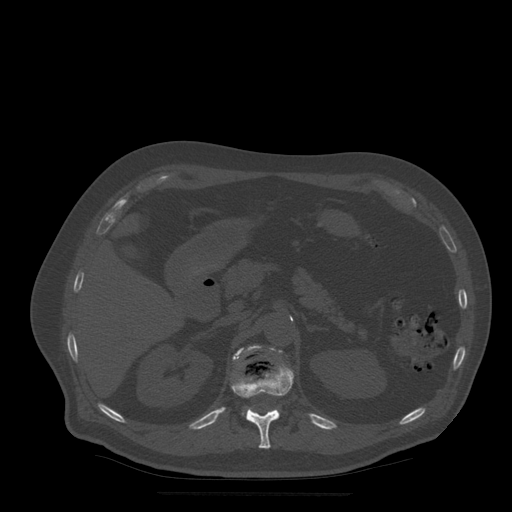
CT including the spine, one axial slice; slice 213 of 522 in the series (ordered by position); bone window (W 1800 / L 400 HU); 1.25 mm slice thickness; 512 × 512 image matrix, field of view 420 × 420 mm. Patient age 72 years. From the clinical record (not read from this slice): primary cancer: prostate.
Structures marked on this image (semi-automatically segmented with operator editing):
- L1 vertebra: box from (x=233, y=346) to (x=282, y=418) px
- T12 vertebra: (x=232, y=364)–(x=294, y=449)